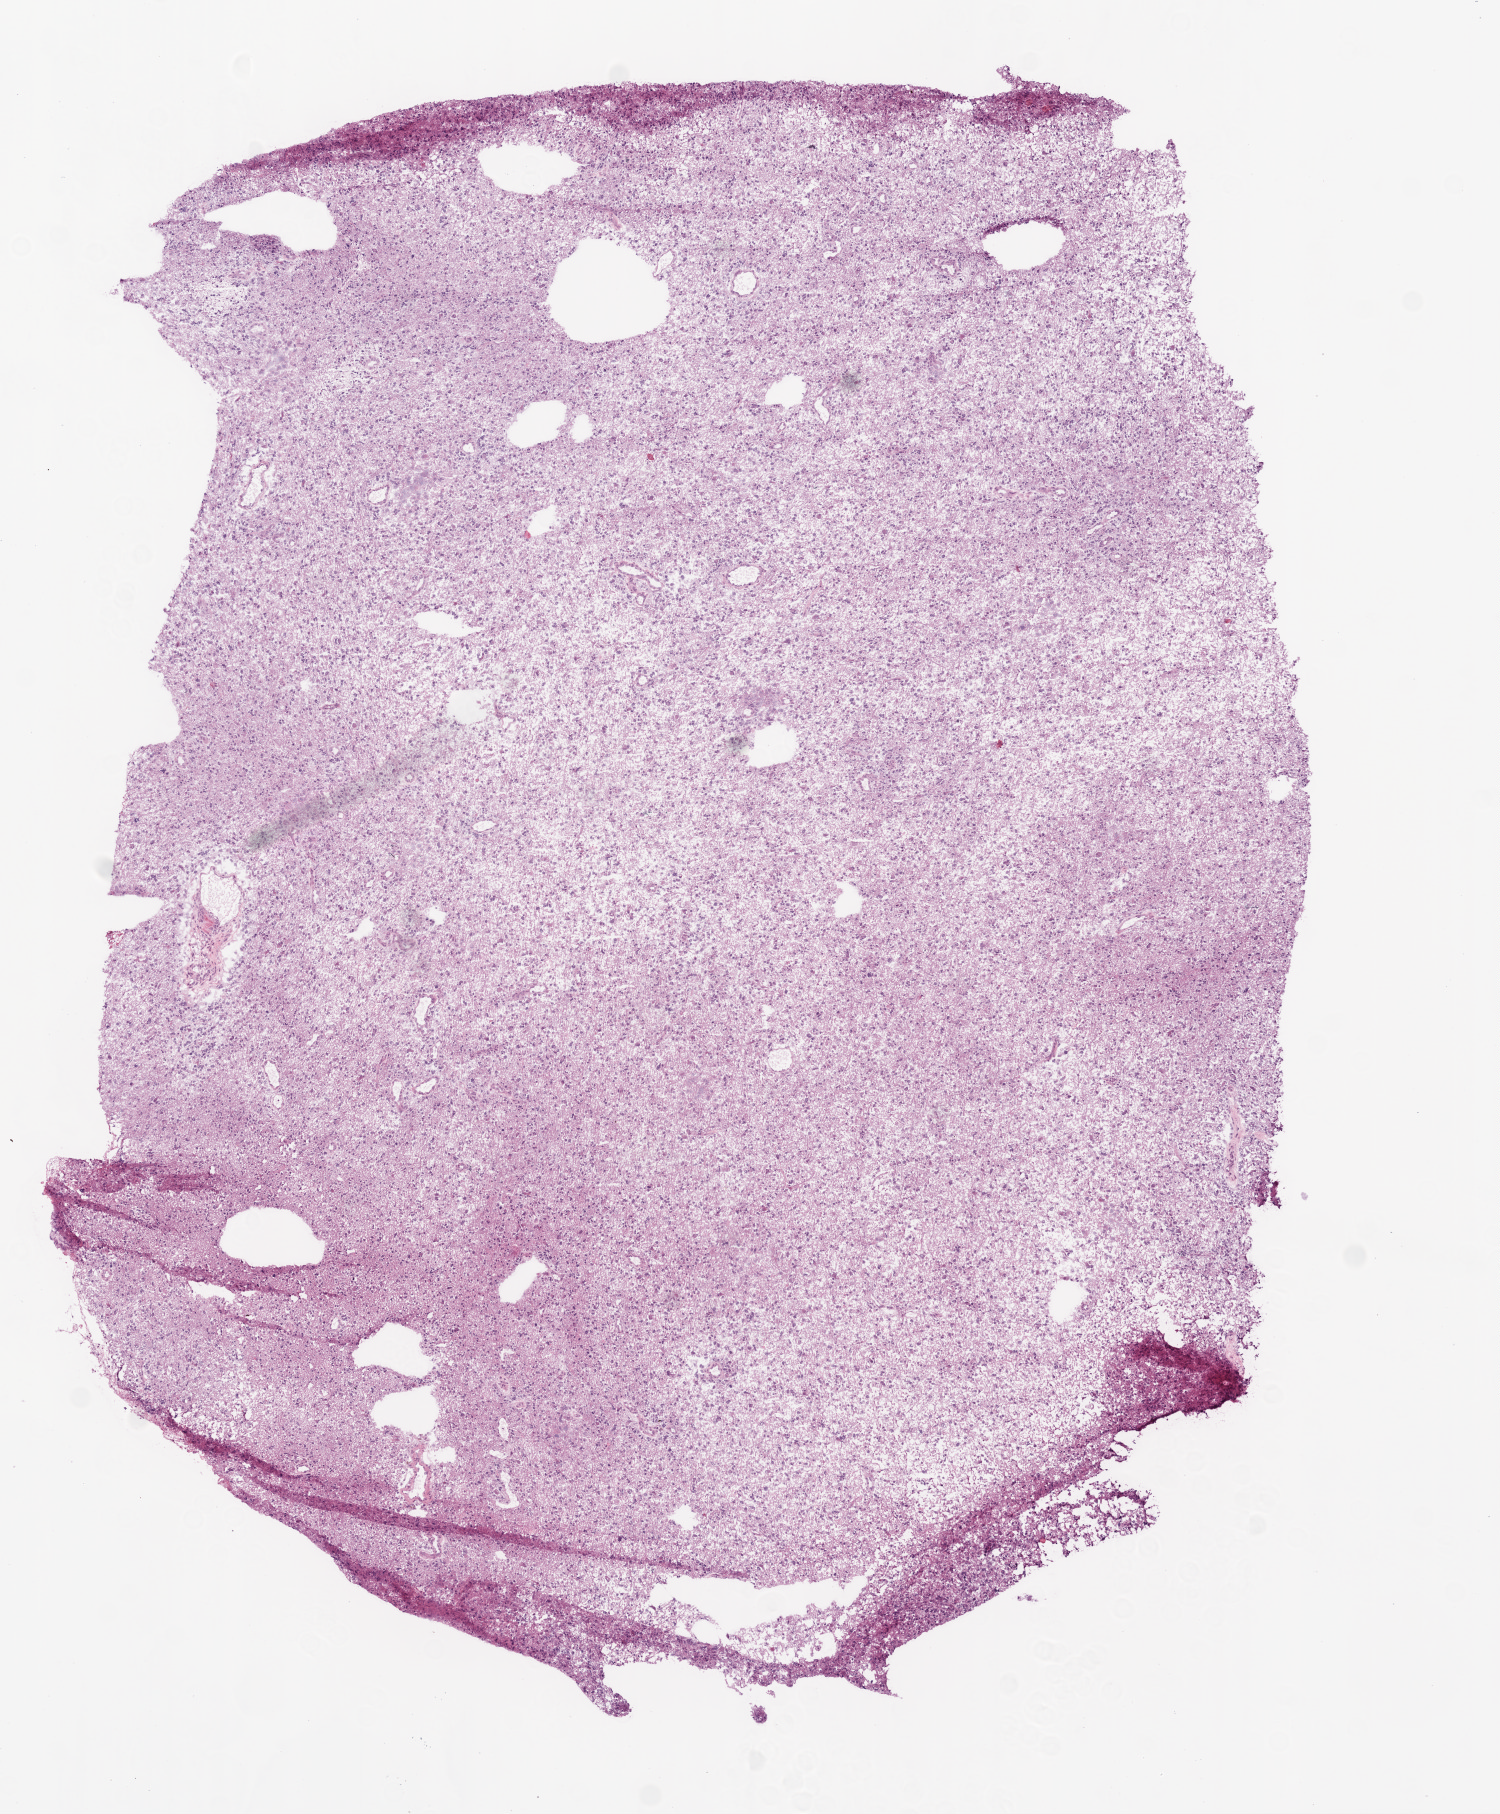
Whole-slide histology image, Hematoxylin and eosin (H&E) stained, low-resolution overview of the scanned area, about 6.0 x 7.3 mm (acquisition: 20x scan). Frozen section from the top of the tissue portion. Primary tumour sample from the brain. Patient: male, age at initial diagnosis 65 years. Pathologist review of this section (percent, as recorded): tumour cells 100%, tumour nuclei 80%, normal cells 0%, stromal cells 0%, necrosis 0%.
Histologic diagnosis: Glioblastoma.